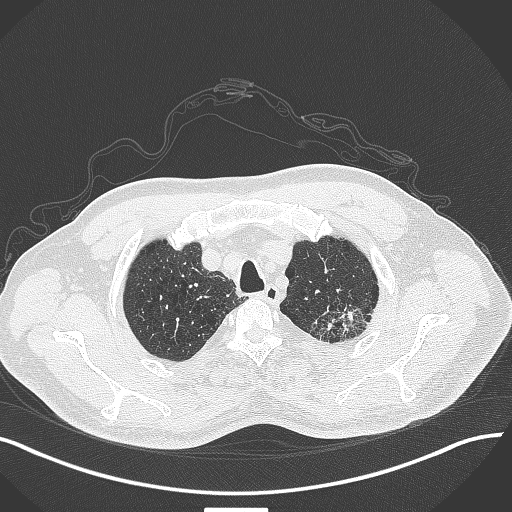
Chest CT, one axial slice. Position 363 of 429 along the scan axis. Reconstruction kernel B70f. Lung window (W 1500 / L -600 HU). 512 × 512 image matrix. Male patient, age 55 years. From the clinical record (not read from this slice): clinical TNM (as recorded): T3 N0 M1c; histopathological grade: G3.
Outlined on this slice (rectangle marked by the reading radiologist):
- lung tumour (recorded histology: adenocarcinoma): bounding box <310,301,376,343> (left, top, right, bottom; pixels)